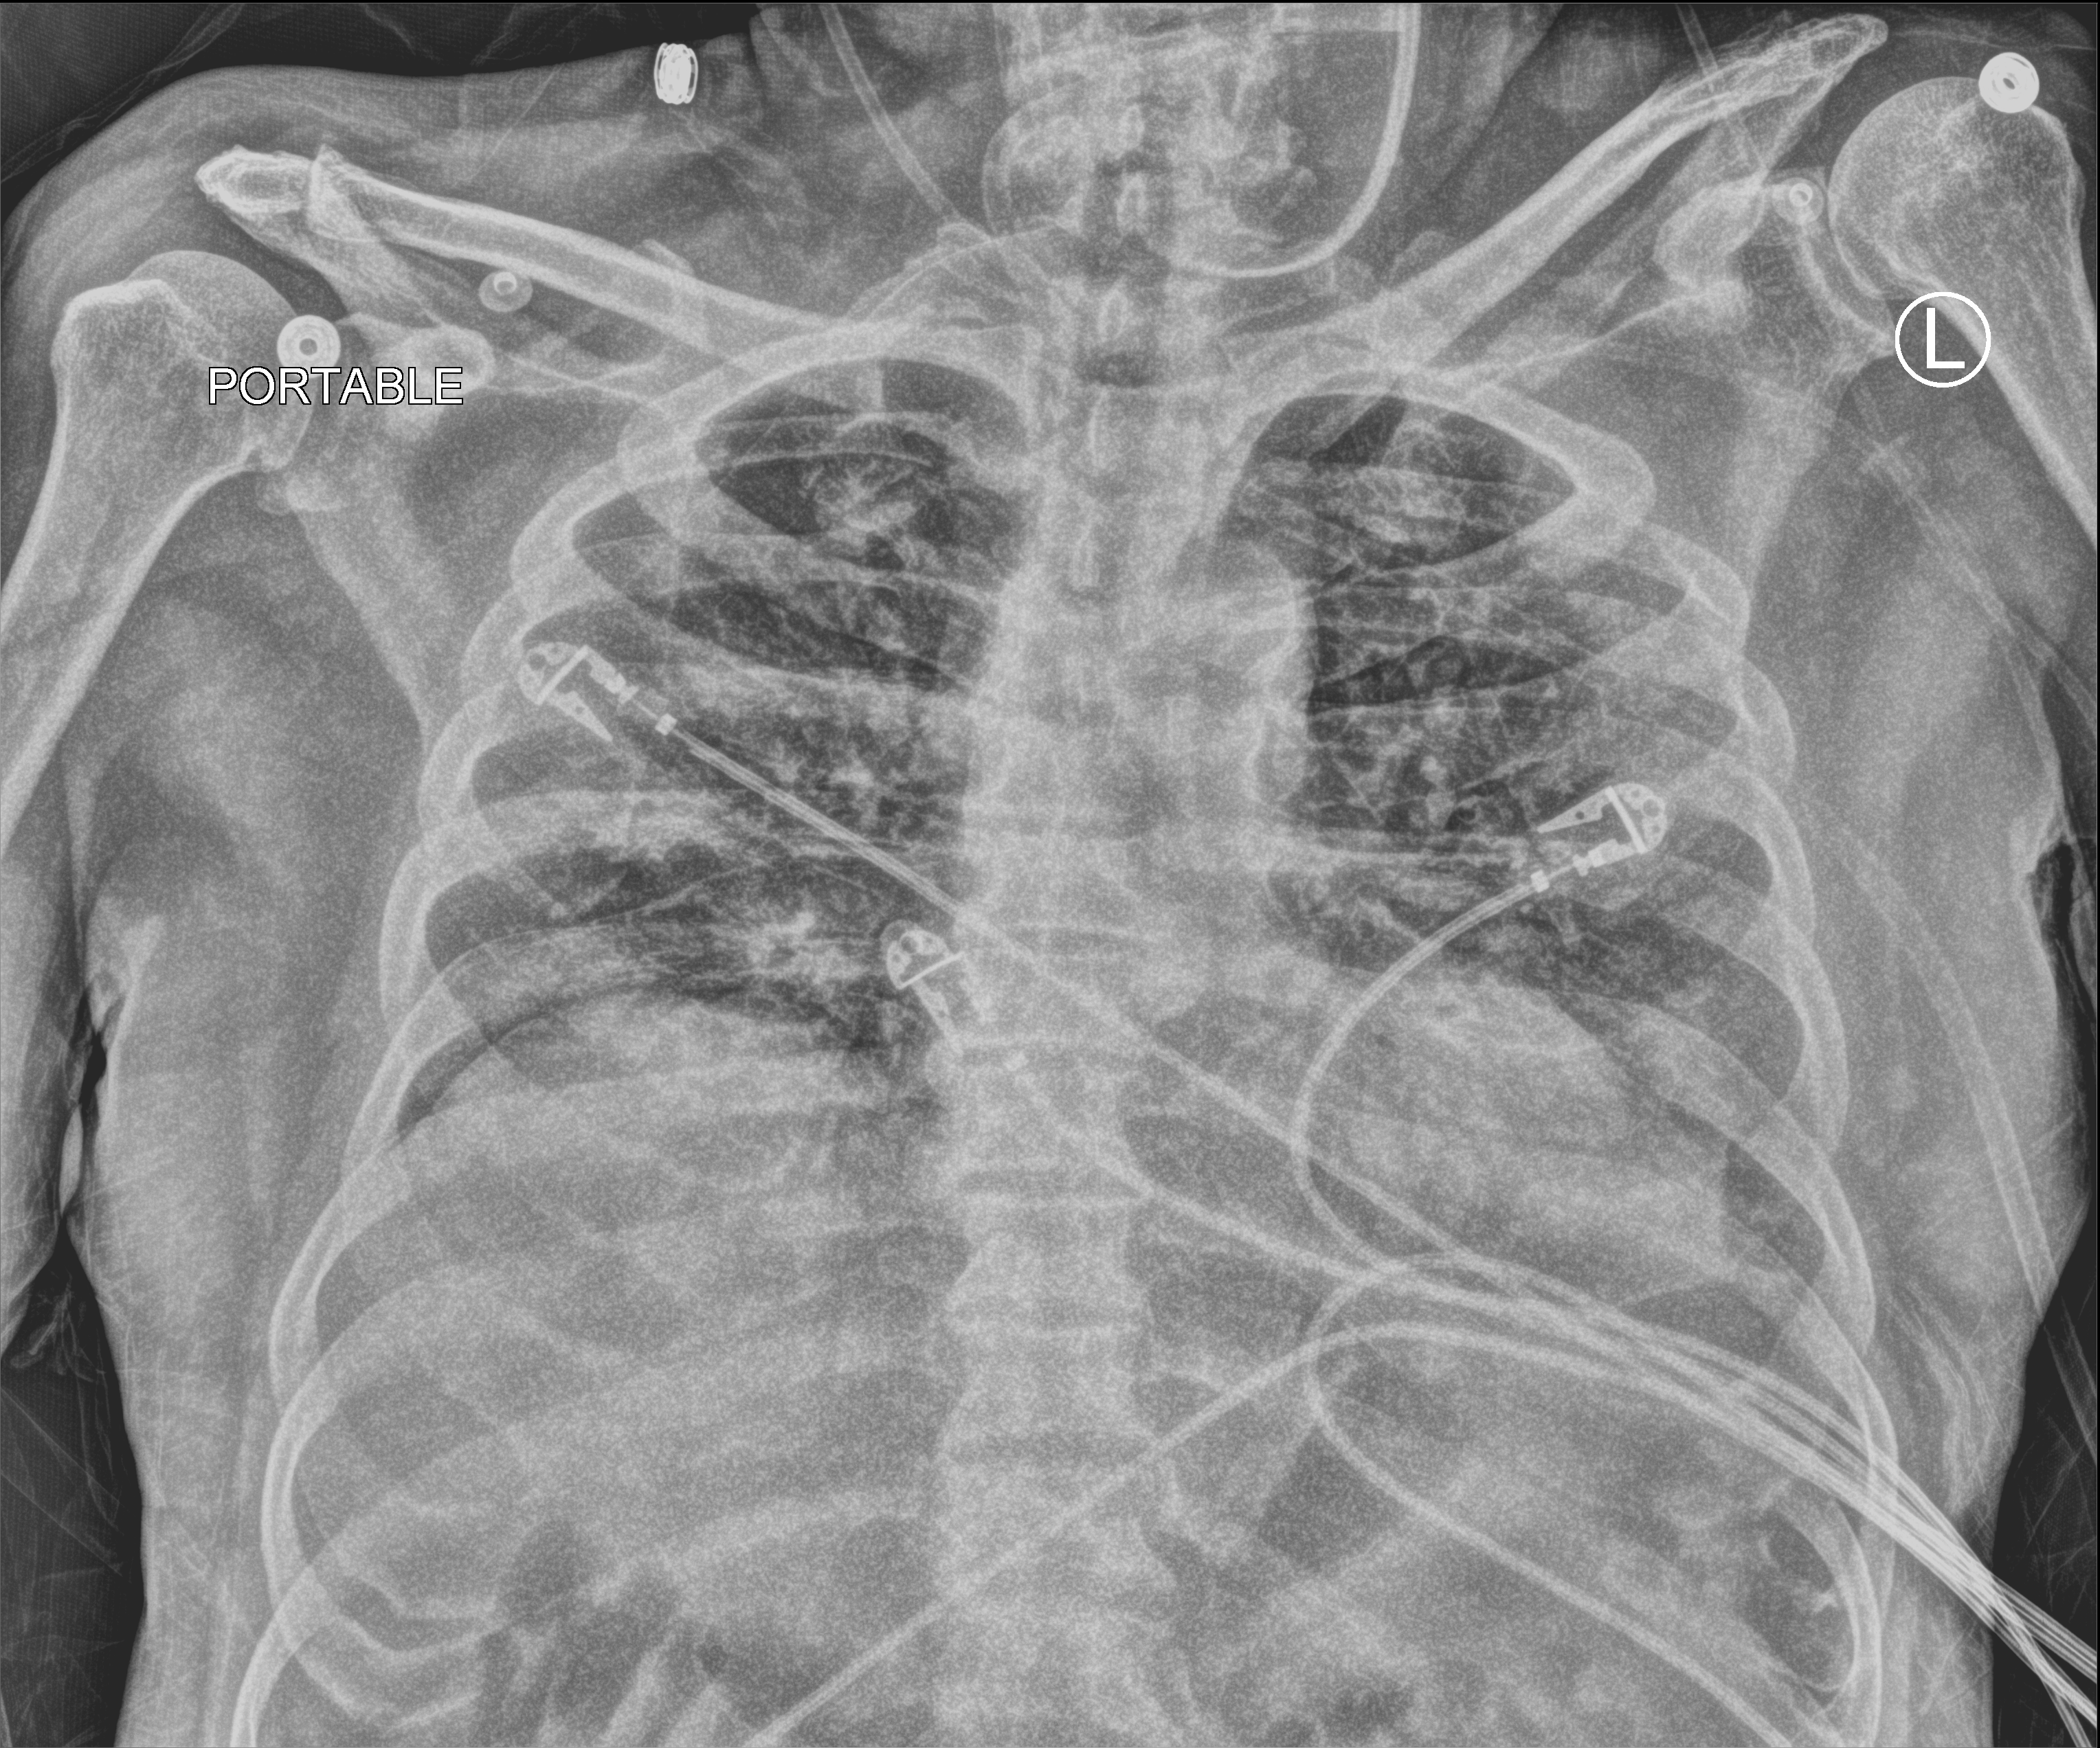
Portable chest radiograph. Patient hospitalised with COVID-19; male, aged 75–90 years.
Hospital-stay facts (about this admission, not read from this image; timing relative to this image not recorded): mechanically ventilated during this hospital stay: yes; admitted to intensive care during this hospital stay: yes.